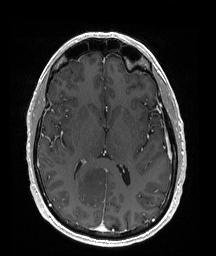
Brain MRI from a brain-tumour surgery series, one axial slice; position 91 of 176 along the scan axis; T1-weighted post-contrast; 1 mm slice thickness; 216 × 256 image matrix. From the clinical record (not read from this slice): histopathology: Oligodendroglioma; WHO grade: 2; IDH mutation: yes.
Annotated regions visible in this slice (expert manual segmentation):
- tumour: bounding box <70,164,111,201> (left, top, right, bottom; pixels)